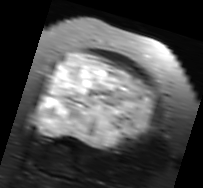
MRI of an extremity soft-tissue mass, one axial slice. Slice 48 of 91 in the series (ordered by position). T2-weighted fat-saturated. MR volume resampled by the dataset authors to the PET/CT grid (not the native acquisition matrix). 3.27 mm slice thickness. 203 × 188 image matrix, field of view 198 × 184 mm. Female patient. From the clinical record (not read from this slice): histological type: malignant solitary fibrous tumor; grade: intermediate; site of the primary tumour: right thigh.
Structures marked on this image (expert contour drawn on MRI and transferred to this co-registered scan by the dataset authors):
- gross tumour volume including surrounding oedema: bounding box [x1, y1, x2, y2] px = [28, 53, 157, 150]
- gross tumour volume (mass): [33, 53, 155, 148]